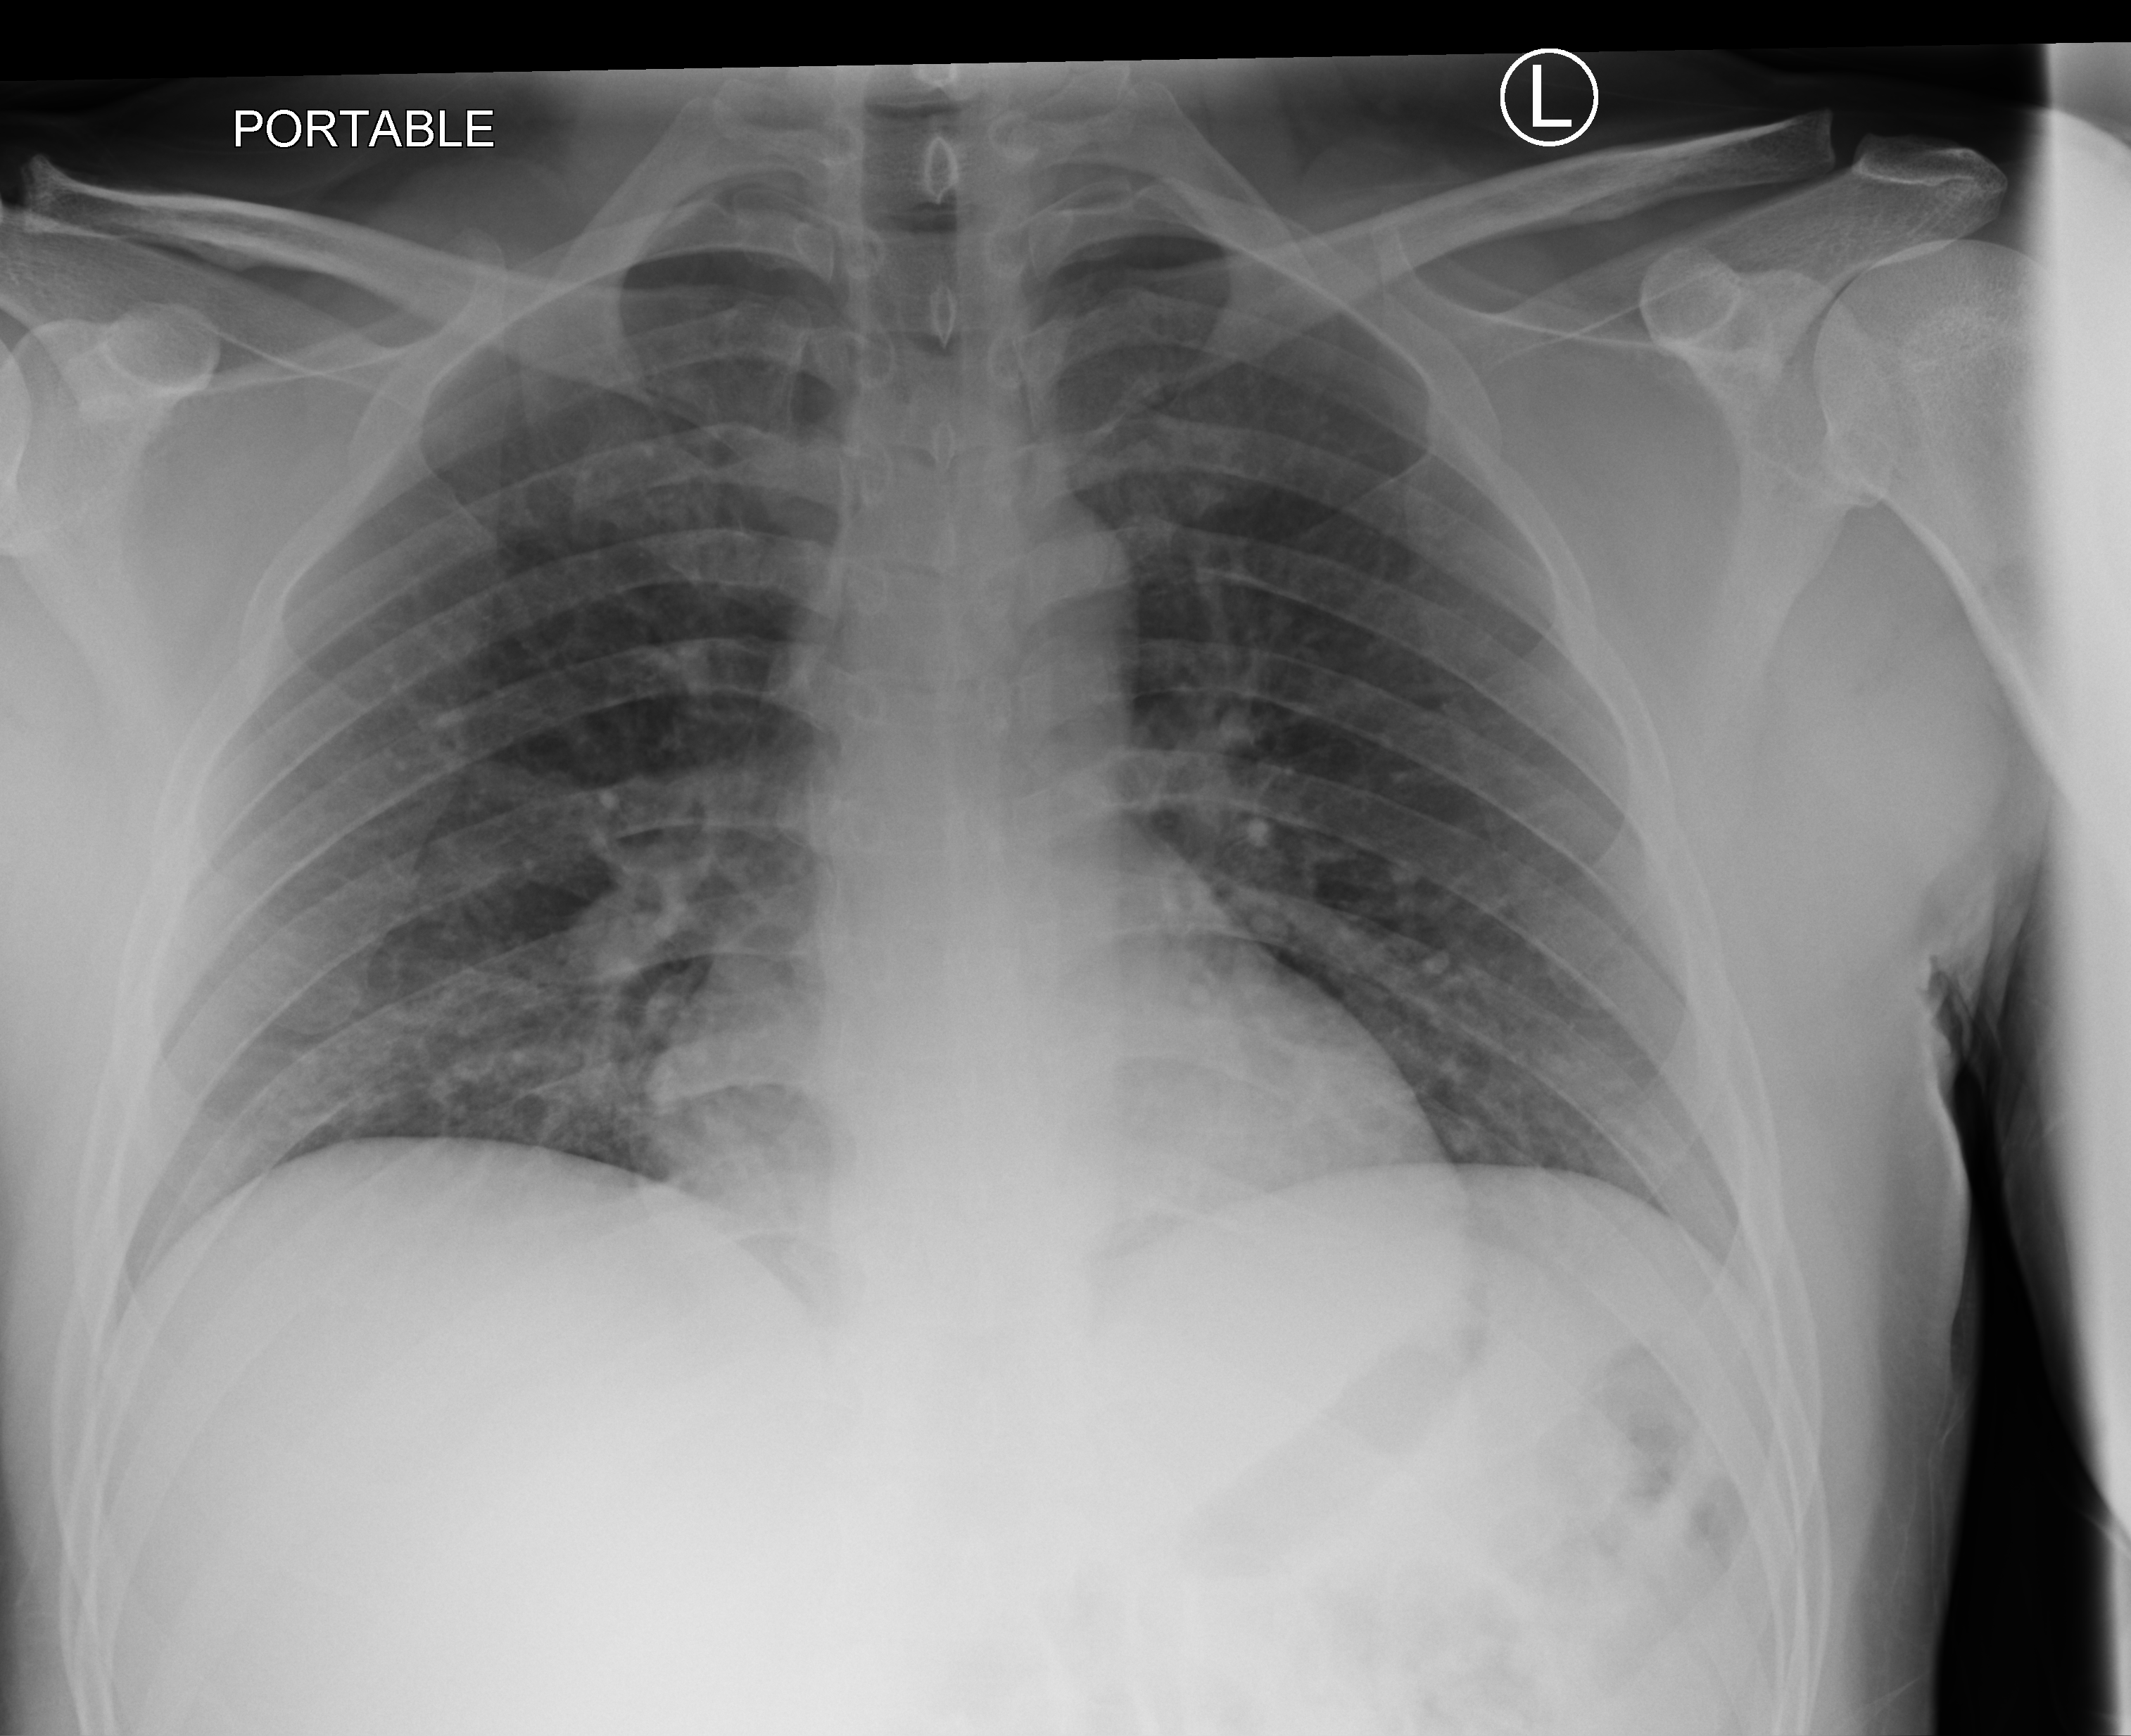
Portable chest radiograph, anteroposterior (AP) projection. Male patient hospitalised with COVID-19, age 18–59 years.
Hospital-stay facts (about this admission, not read from this image; timing relative to this image not recorded): admitted to intensive care during this hospital stay: no.